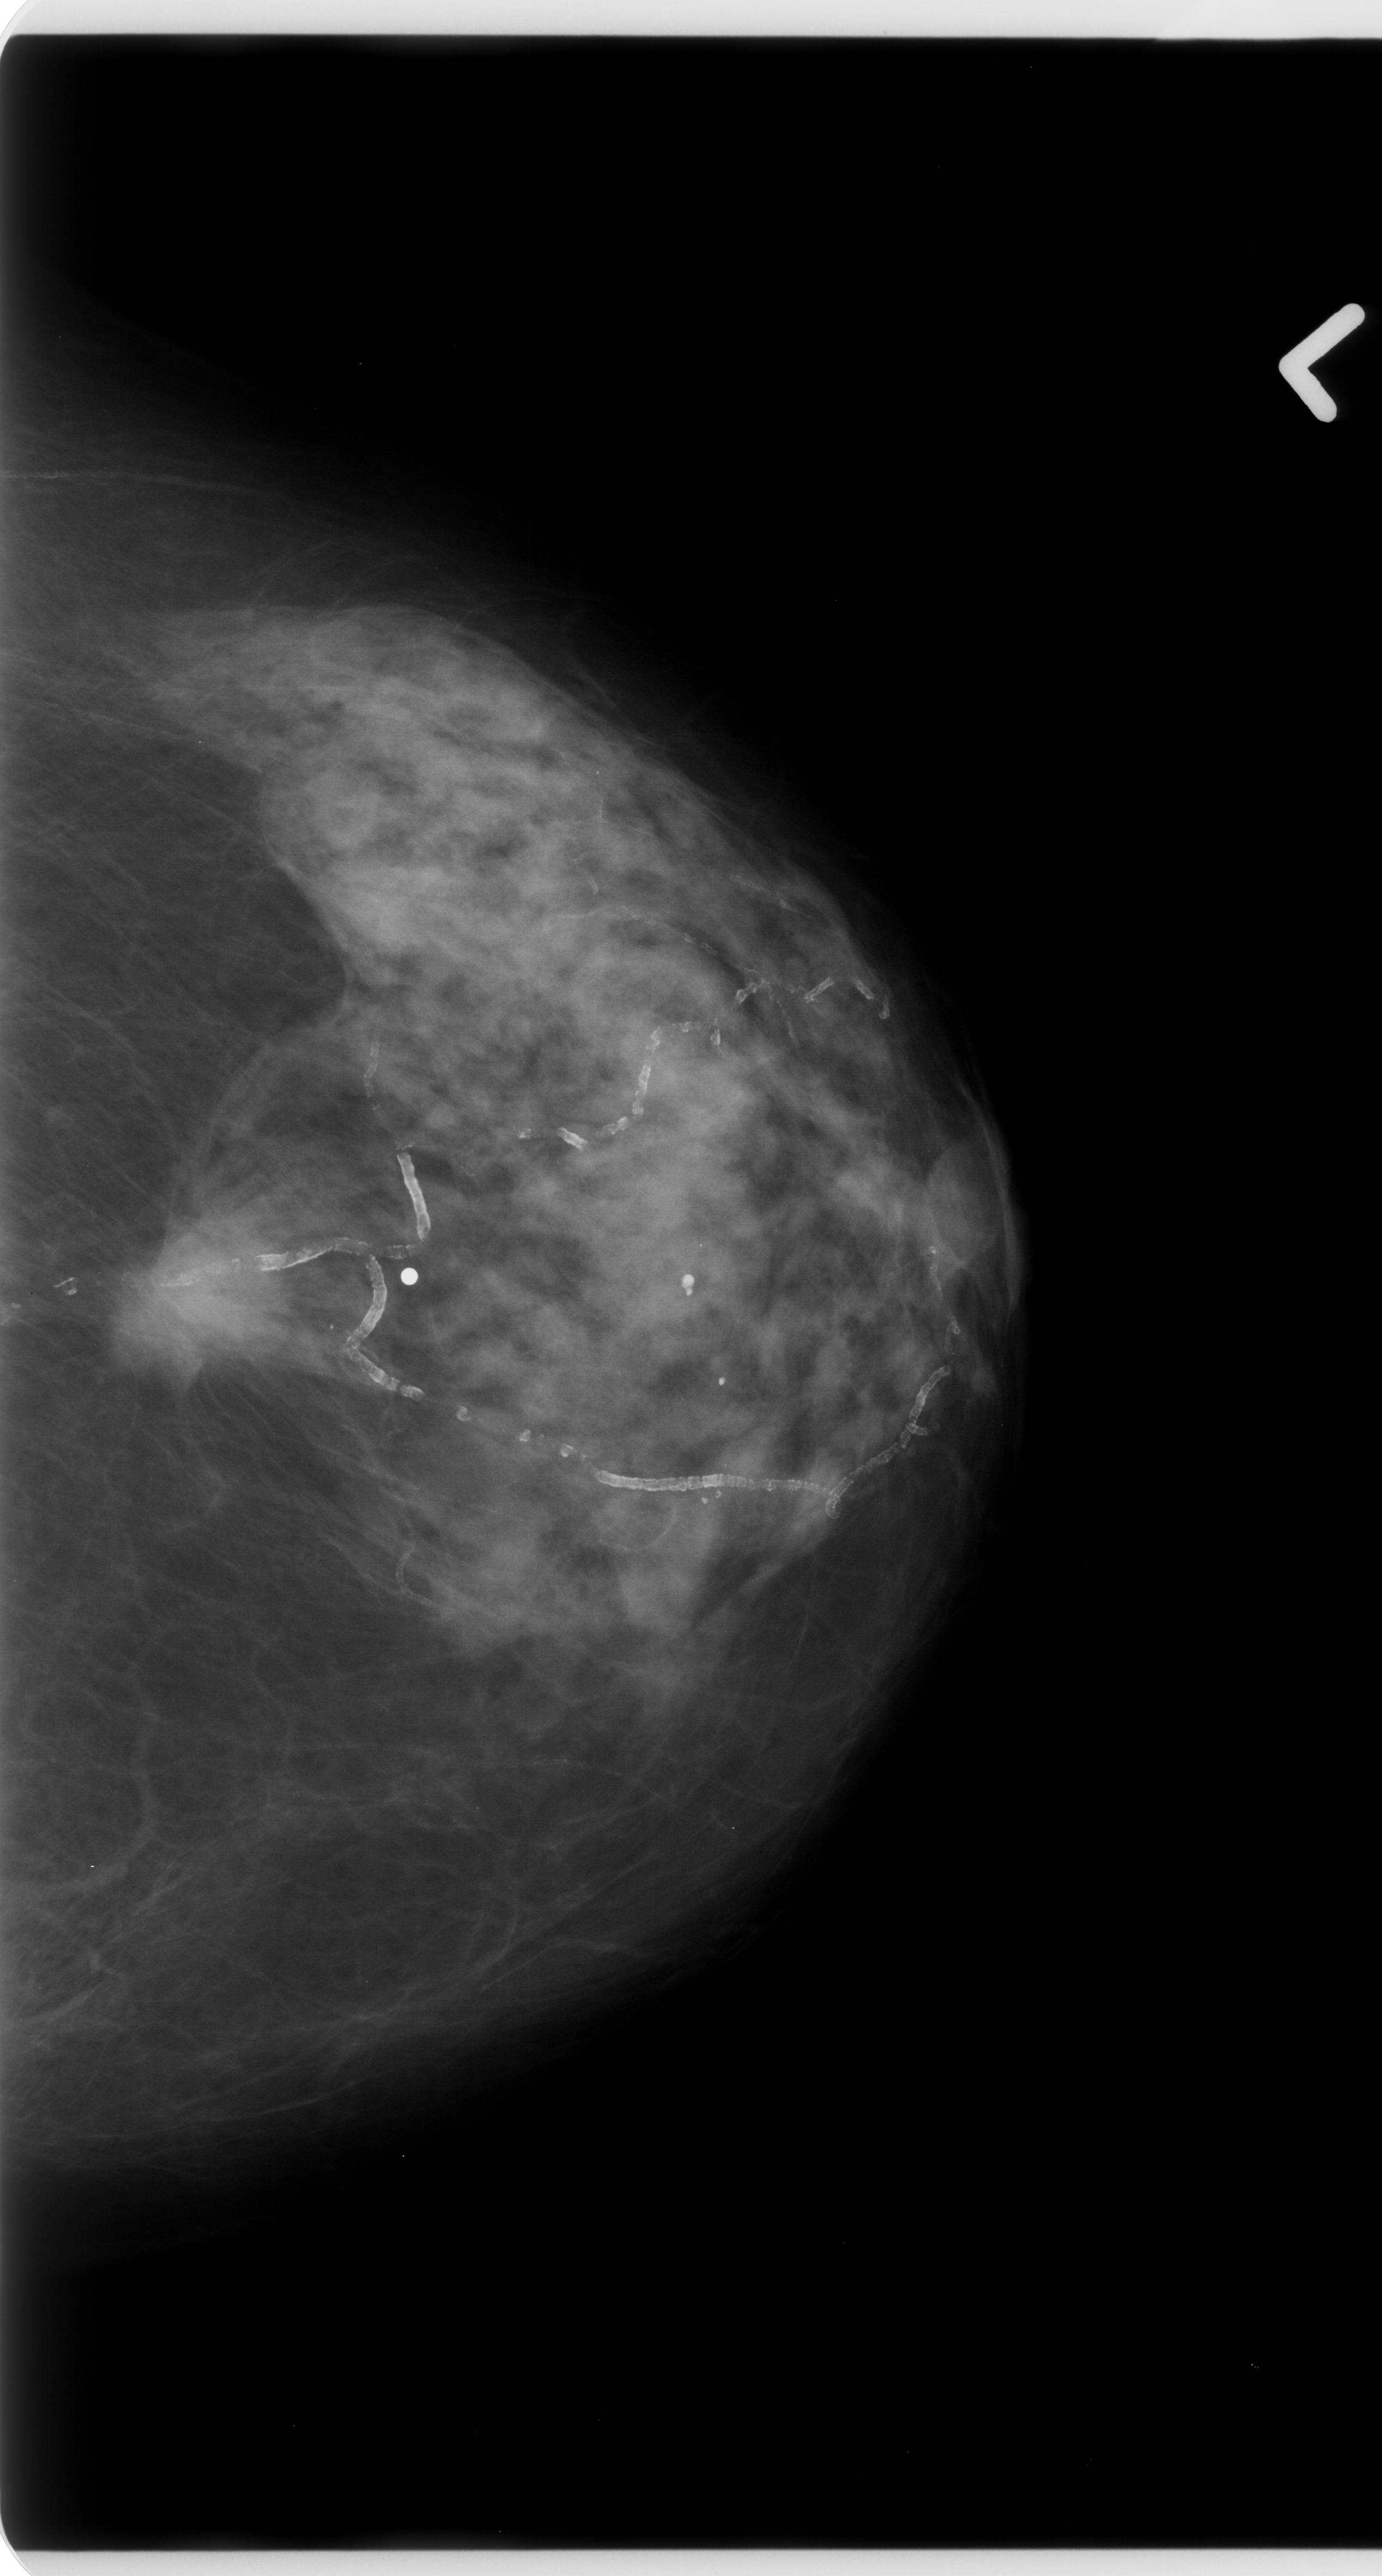
Digitized screen-film mammogram; left breast; craniocaudal (CC) view; 1382 × 2576 image matrix.
Marked abnormalities (boxes around the expert regions of interest):
- mass, shape oval, margins spiculated; BI-RADS assessment category 5; subtlety rating 5 on a 1 (subtle) to 5 (obvious) scale; pathology result (as recorded, not read from the image): malignant: bounding box [x1, y1, x2, y2] px = [114, 1176, 359, 1388]